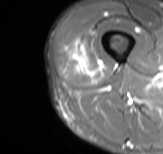
MRI of an extremity soft-tissue mass, one axial slice; slice 15 of 61 in the series (ordered by position); STIR; MR volume resampled by the dataset authors to the PET/CT grid (not the native acquisition matrix); 163 × 154 image matrix, field of view 159 × 150 mm. Male patient. Case-level facts recorded for this patient, not image findings: histological type: poorly differentiated synovial sarcoma; grade: high; site of the primary tumour: right buttock.
Structures marked on this image (expert contour drawn on MRI and transferred to this co-registered scan by the dataset authors):
- gross tumour volume including surrounding oedema: box from (x=68, y=41) to (x=102, y=76) px